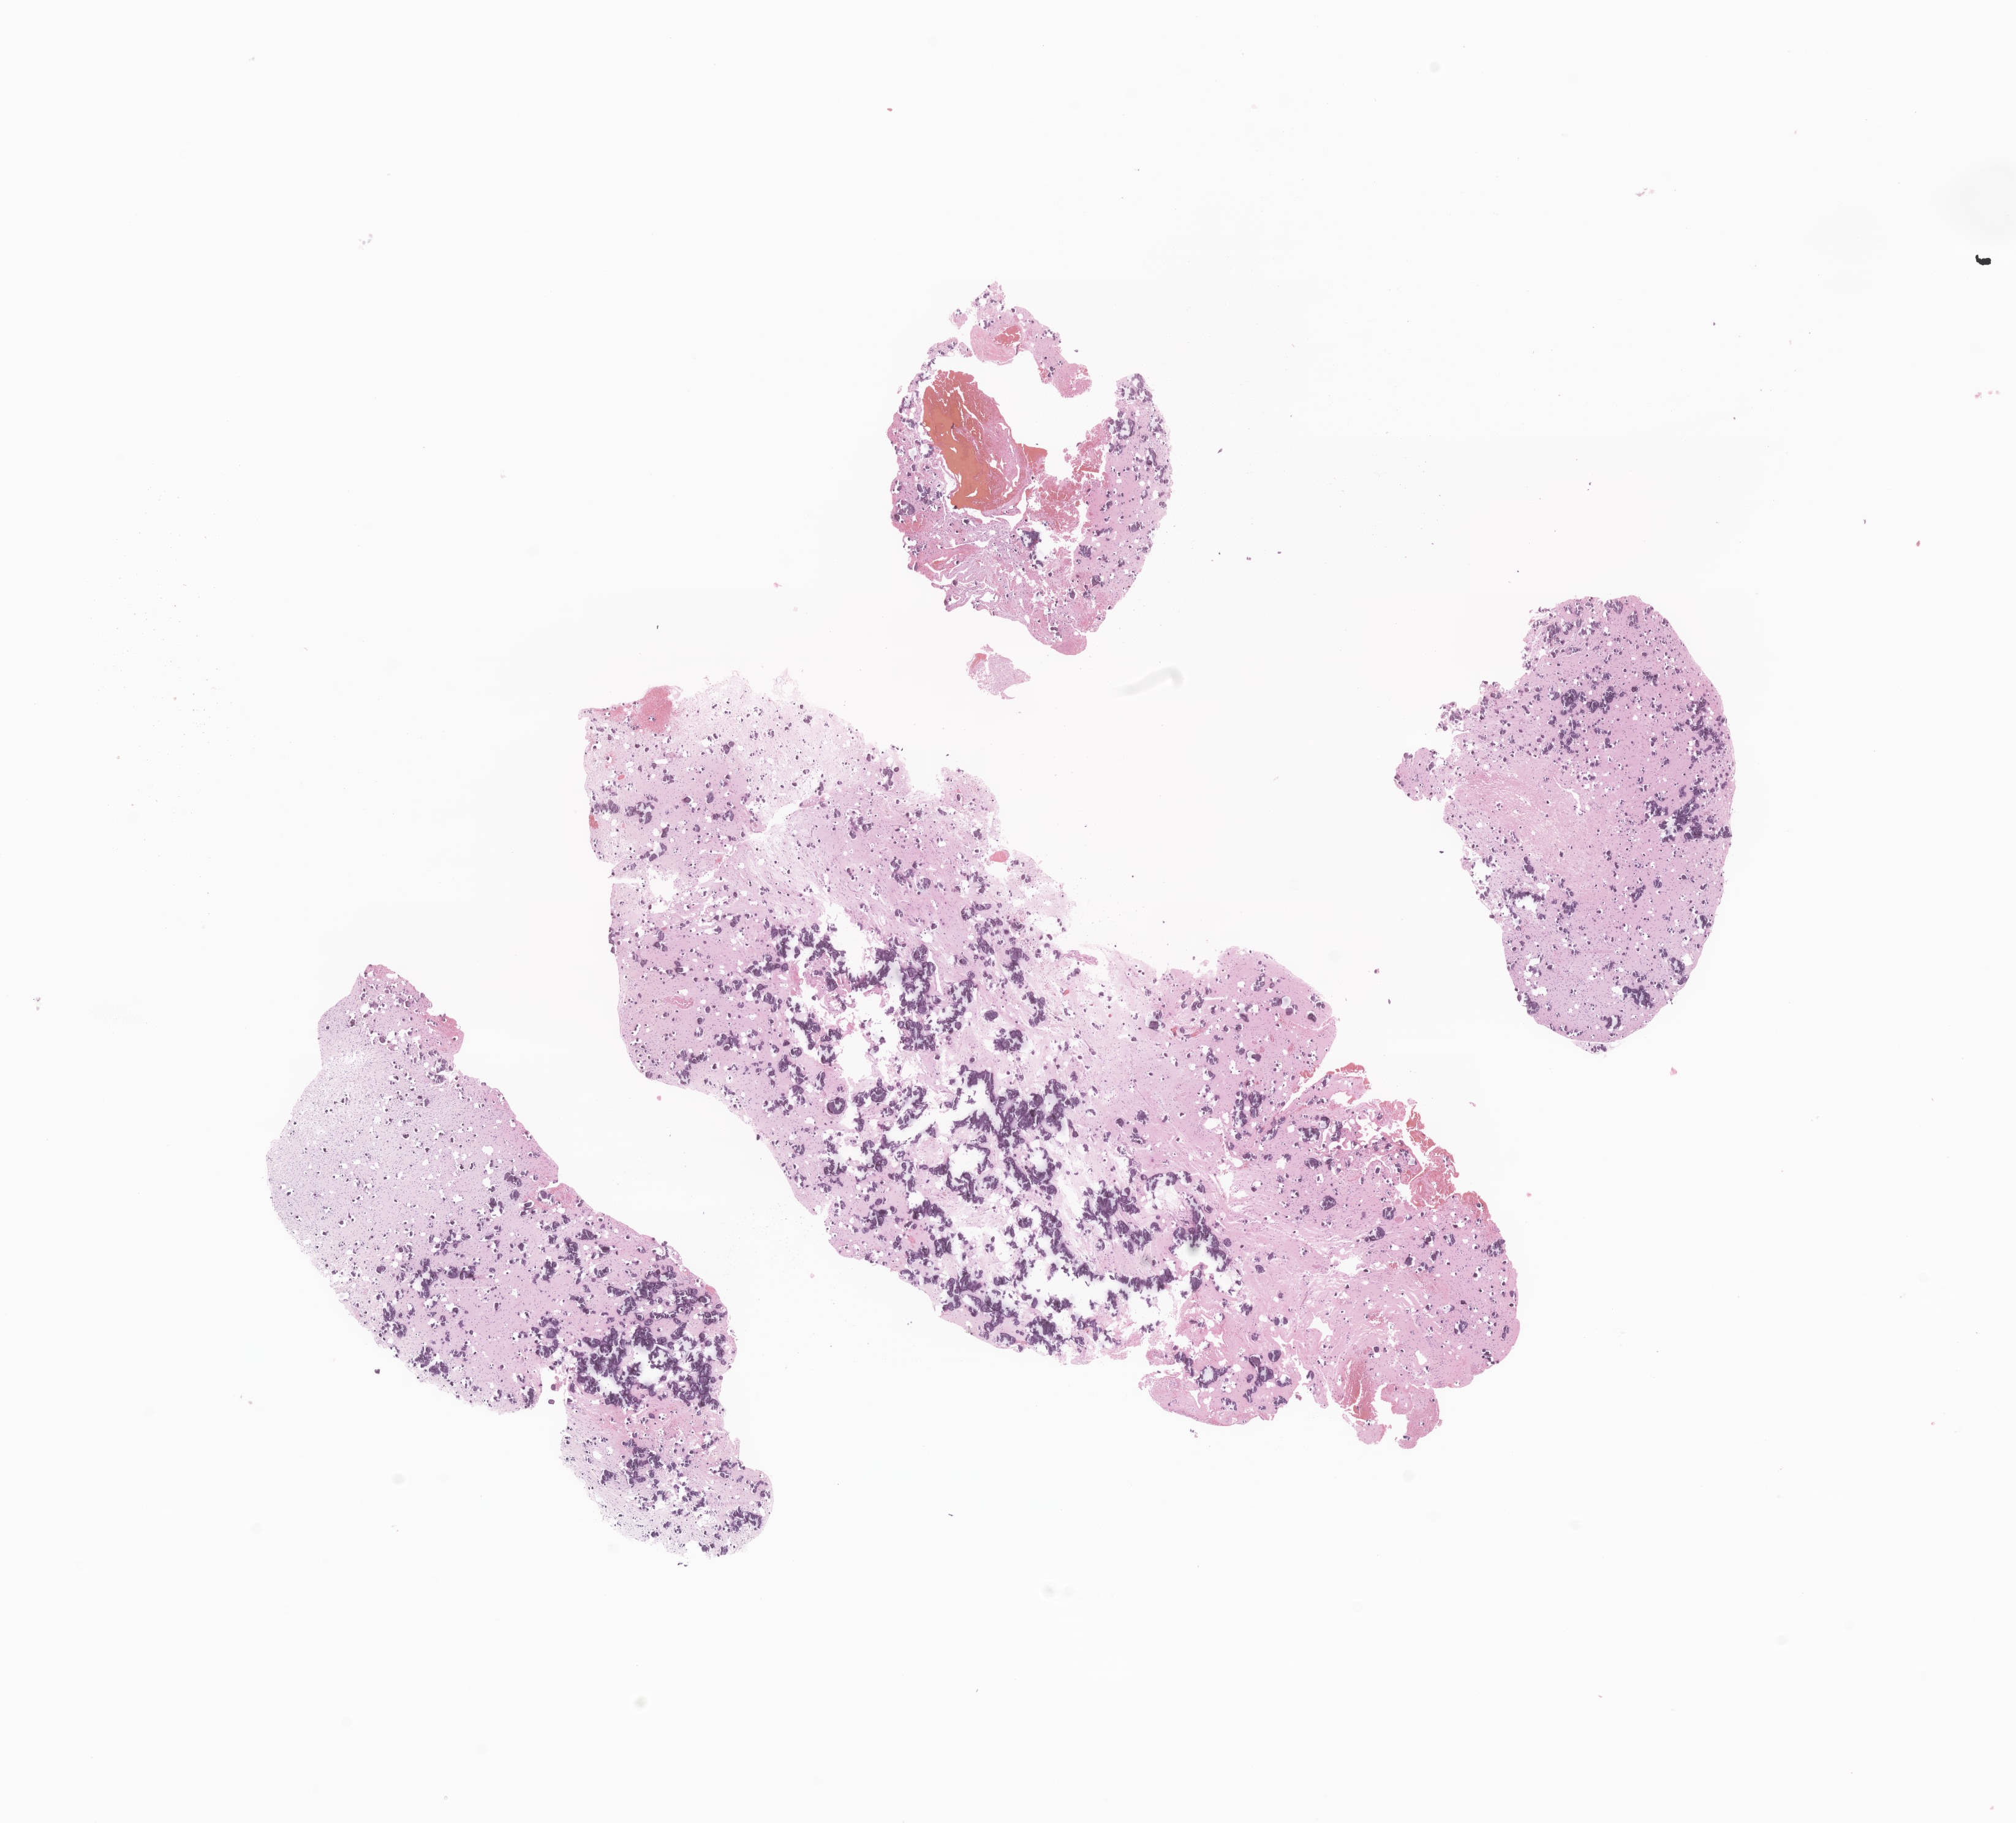
Whole-slide image, haematoxylin and eosin stain of tumor tissue from the brain — whole scanned area (about 13.9 x 12.5 mm) shown as a low-resolution overview. Formalin-fixed, paraffin-embedded (FFPE) tissue. Patient male; age 231 months (19 years 3 months).
• diagnosis: Neoplasm, benign